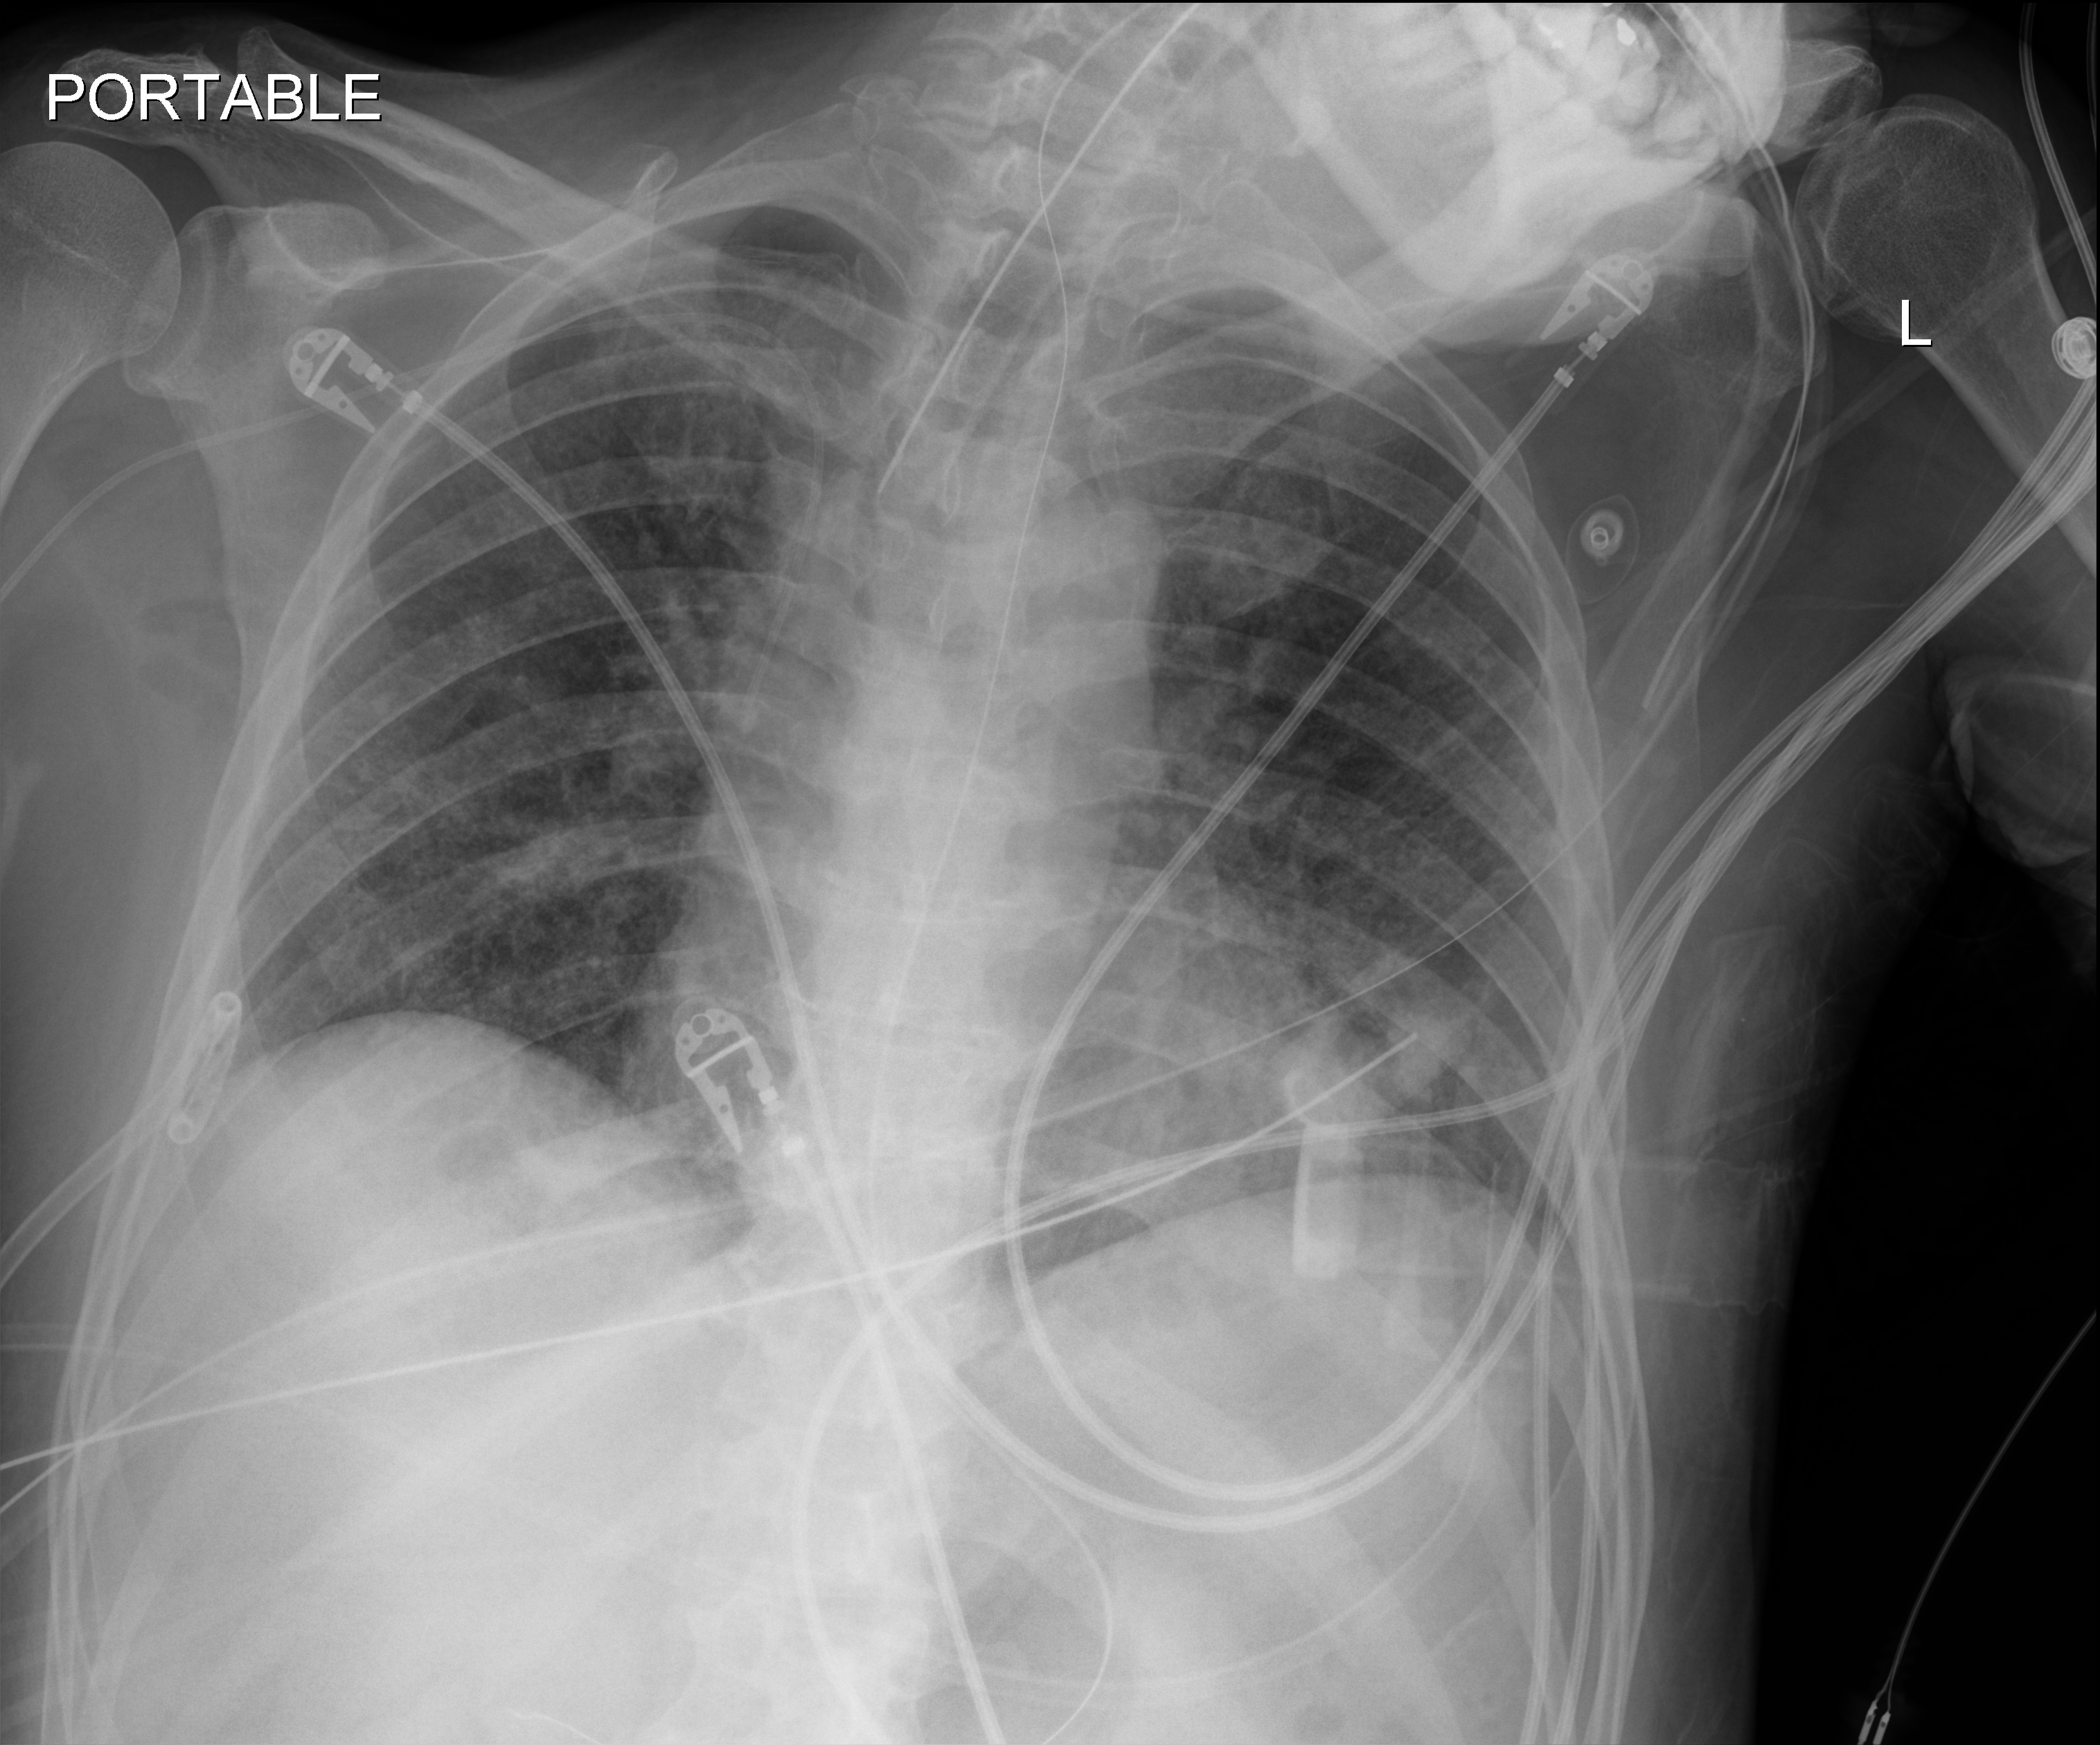
Bedside chest radiograph (digital radiography); anteroposterior (AP) projection. Patient hospitalised with COVID-19; male, aged 18–59 years.
From the hospital-stay record, not from the radiograph (when in the stay this image was taken is not recorded): smoking status (admission record): never; admitted to intensive care during this hospital stay: yes; mechanically ventilated during this hospital stay: yes.